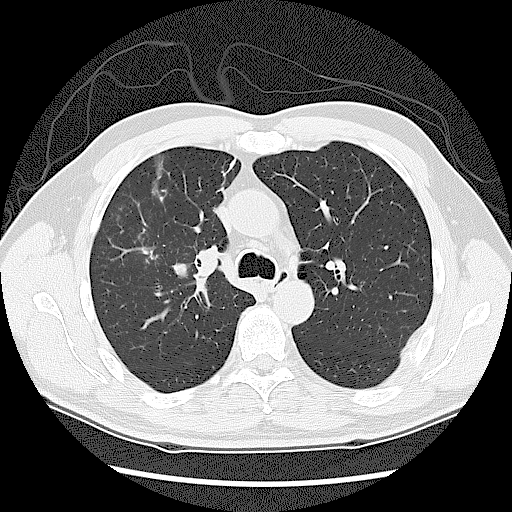
Axial slice from a low-dose chest CT screening exam. First (baseline) screen. Lung window (W 1500 / L -600 HU). 2.5 mm slice thickness. Slice 46 of 131 in the series. 512 × 512 image matrix. Male participant, aged 60 years at enrolment. Current smoker at enrolment.
• Expert-annotated lung lesion, bounding box <158,223,244,319> (left, top, right, bottom; pixels).
• Screening reader's record for this exam: no non-calcified nodule ≥4 mm recorded.
• Official screen result: negative screen, significant abnormalities not suspicious for lung cancer.
• Participant outcome: lung cancer diagnosed 41 days after this screen — small cell carcinoma, NOS, right upper lobe, stage IIIA (AJCC 6th edition).